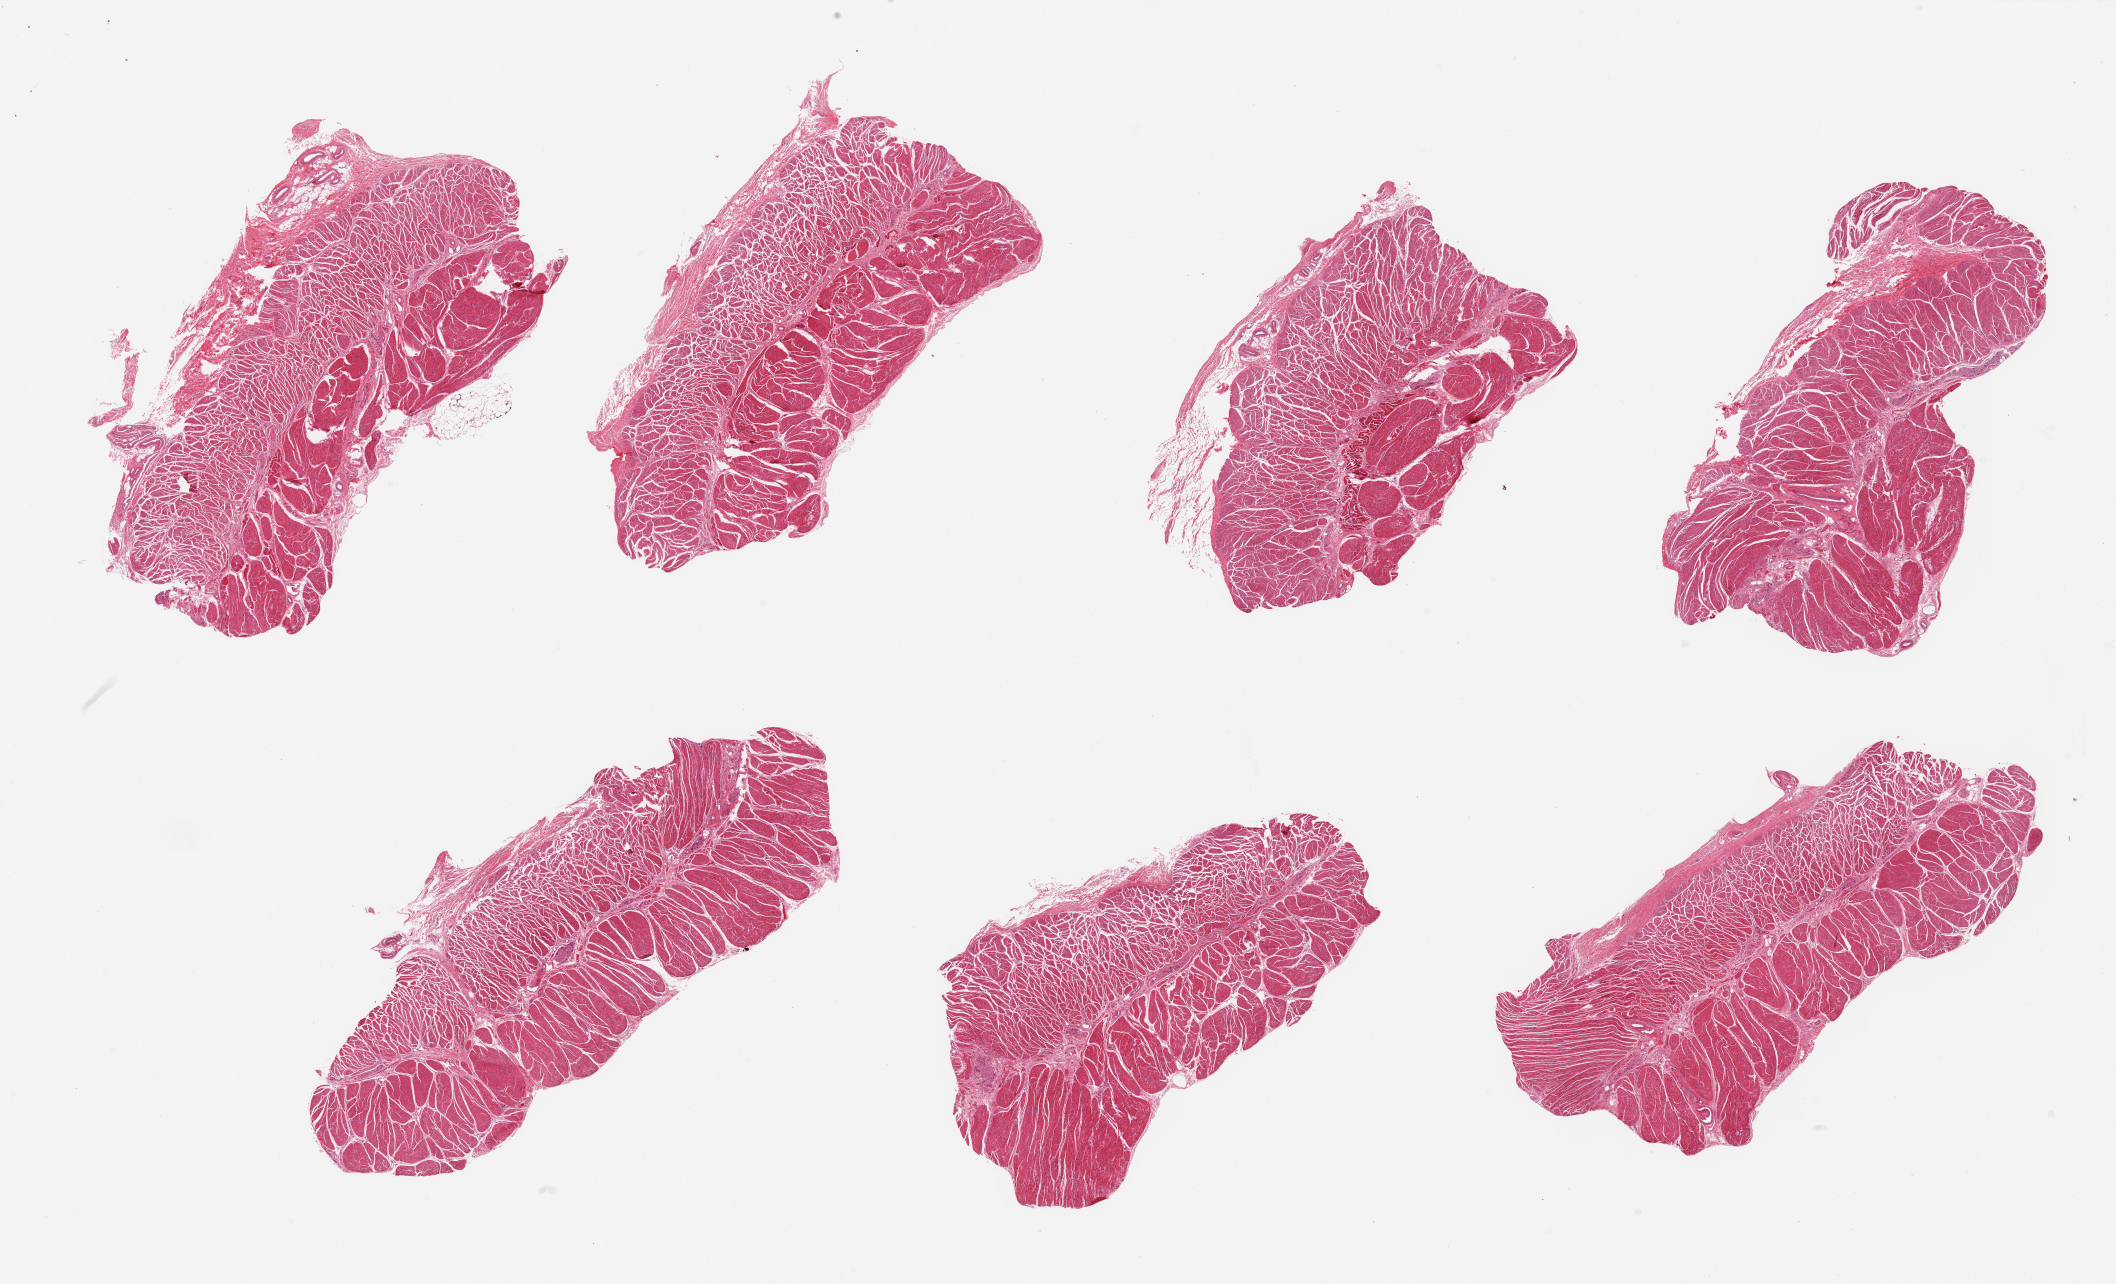
H&E whole-slide image, brightfield, shown as a low-resolution overview of the whole scanned area (about 33.5 x 20.3 mm, acquisition: 20x scan); PAXgene-fixed, paraffin-embedded tissue; target tissue: esophageal muscle; tissue donor sample.
* pathologist's review note for this sample: 7 pieces; well dissected